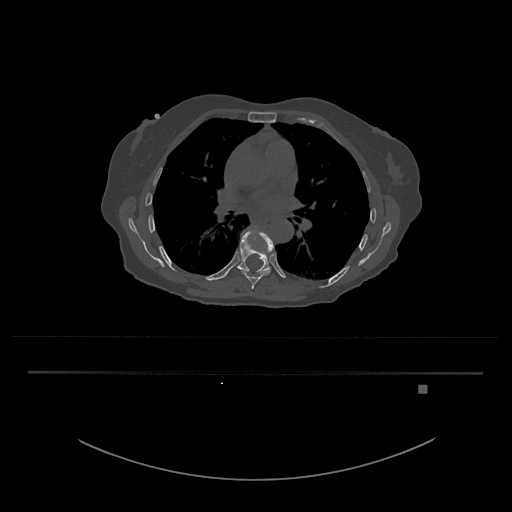
CT including the spine, one axial slice. Slice 783 of 797 in the series (ordered by position). 120 kVp. Bone window (W 1800 / L 400 HU). 512 × 512 image matrix, field of view 500 × 500 mm. Female patient, age 57 years. Case-level facts recorded for this patient, not image findings: primary cancer: cervical.
Annotated regions visible in this slice (semi-automatic segmentation, software-assisted and operator-edited):
- T8 vertebra: bounding box <239,231,274,289> (left, top, right, bottom; pixels)
- T9 vertebra: <225,228,273,278>